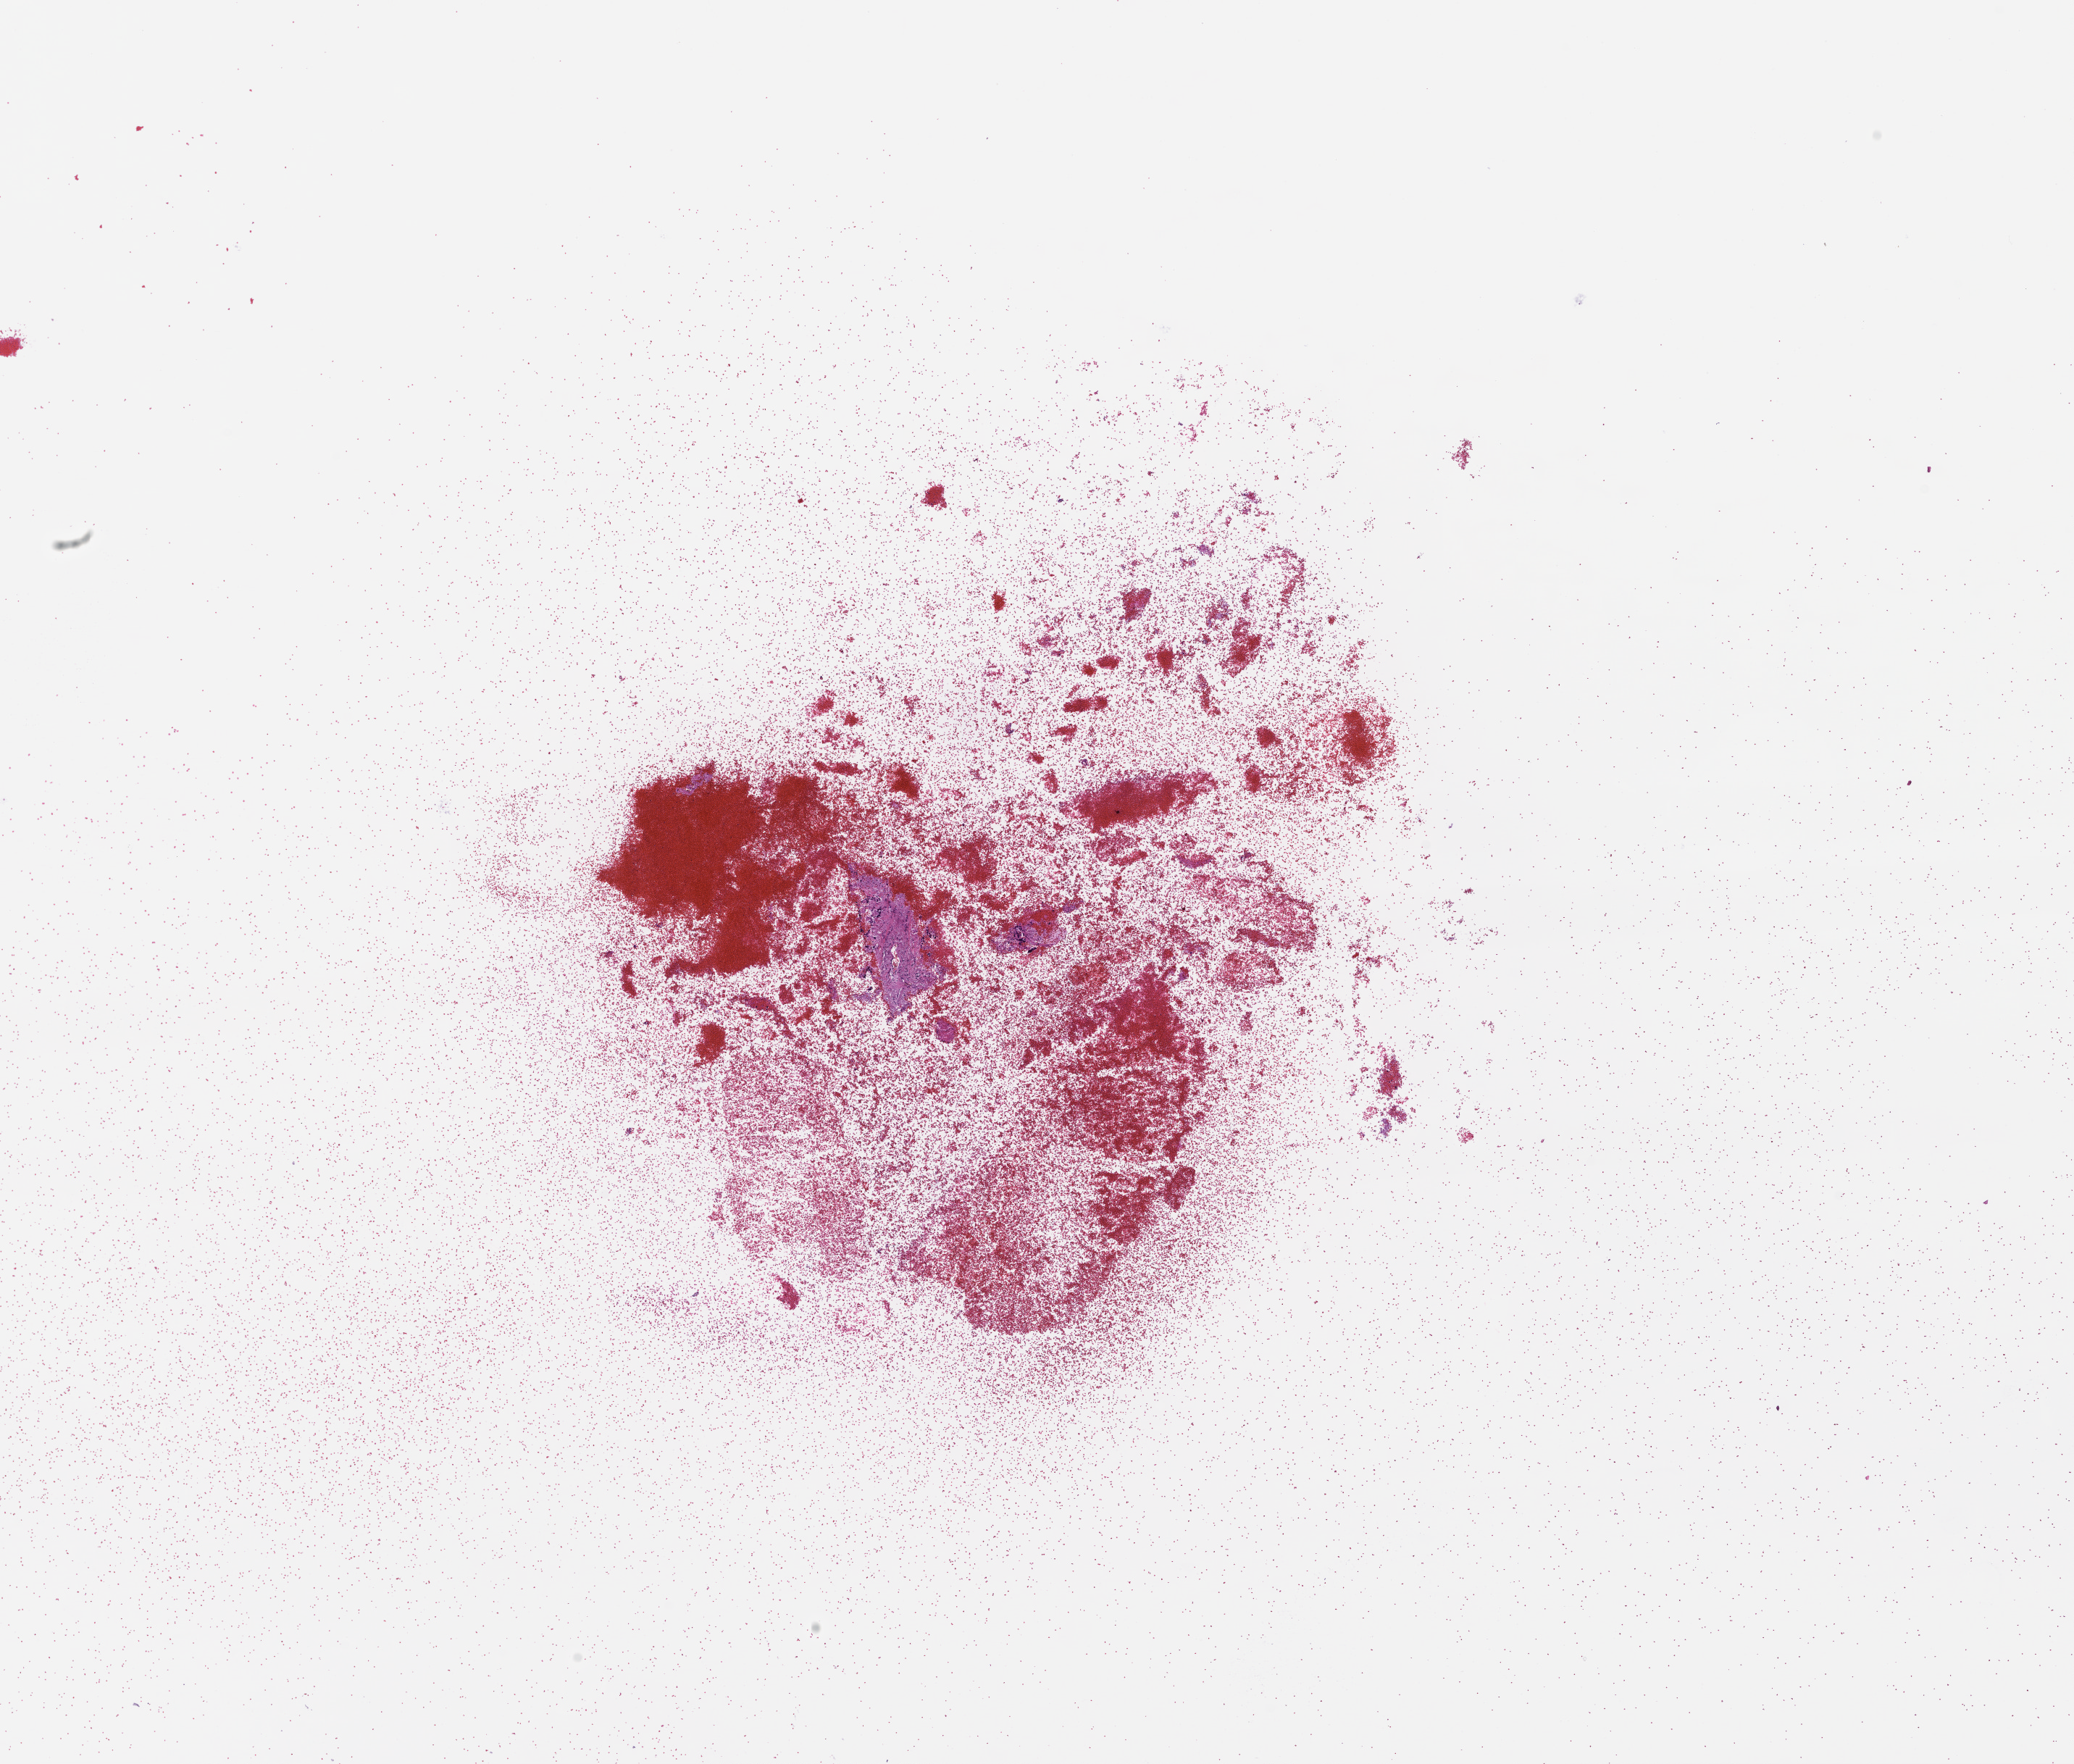
Whole-slide image, hematoxylin and eosin (H&E) stain — shown as a low-resolution overview of the whole scanned area (about 11.6 x 9.8 mm), formalin-fixed, paraffin-embedded (FFPE) tissue, archival tissue. Female patient.
* this section: metastasis (sampled organ not recorded)
* primary diagnosis of the patient: Colorectal Carcinoma